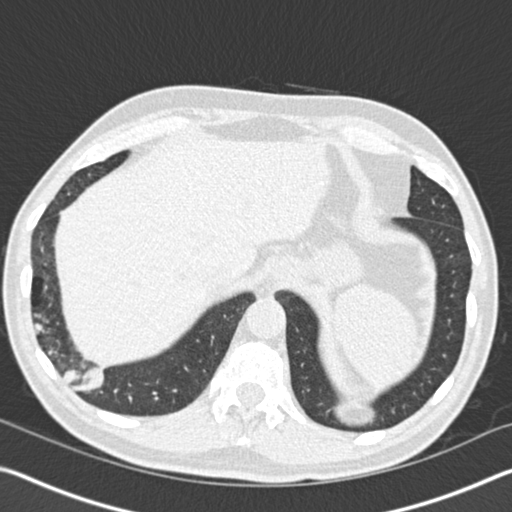
Axial slice from a low-dose chest CT screening exam; first (baseline) screen; lung window (W 1500 / L -600 HU); 2 mm slice thickness; standard (soft-tissue) reconstruction kernel (B30f); slice 129 of 161 in the series. Male participant, aged 61 years at enrolment.
Expert-annotated lung lesion, bounding box (x1, y1, x2, y2) in pixels: (4, 266, 134, 413). Screening reader's record for this exam (one nodule recorded; not confirmed to be the boxed lesion): non-calcified nodule or mass ≥4 mm, right lower lobe, 52 × 36 mm, spiculated (stellate) margins, soft tissue attenuation.